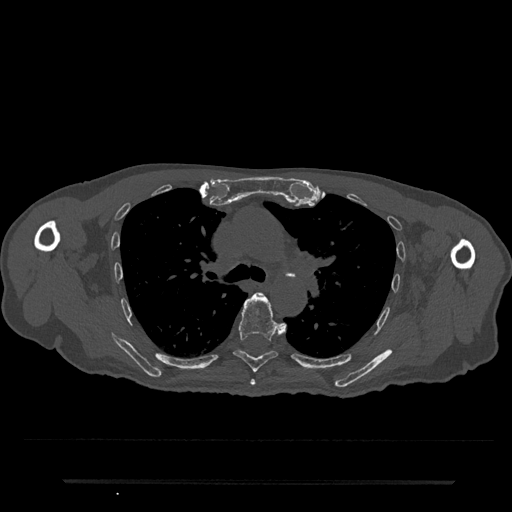
CT including the spine, one axial slice; position 531 of 797 along the scan axis; 120 kVp; bone window (W 1800 / L 400 HU); 0.5 mm slice thickness; 512 × 512 image matrix, field of view 427 × 427 mm. Patient: male, 74 years. Case-level facts recorded for this patient, not image findings: primary cancer: prostate.
Structures marked on this image (semi-automatic segmentation, software-assisted and operator-edited):
- T5 vertebra: bounding box <250,379,256,386> (left, top, right, bottom; pixels)
- T6 vertebra: <233,292,282,373>